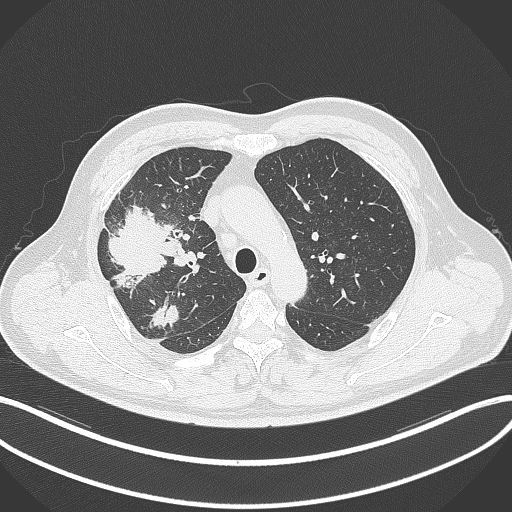
Chest CT, one axial slice; slice 241 of 348 in the series (ordered by position); reconstruction kernel B70f; 120 kVp; lung window (W 1500 / L -600 HU); 1 mm slice thickness; 512 × 512 image matrix, field of view 400 × 400 mm. Patient: male, 55 years. Case-level facts recorded for this patient, not image findings: clinical TNM (as recorded): T3 N2 M1.
Annotated regions visible in this slice (bounding box drawn by a radiologist):
- lung tumour (recorded histology: adenocarcinoma): box from (x=96, y=202) to (x=179, y=294) px